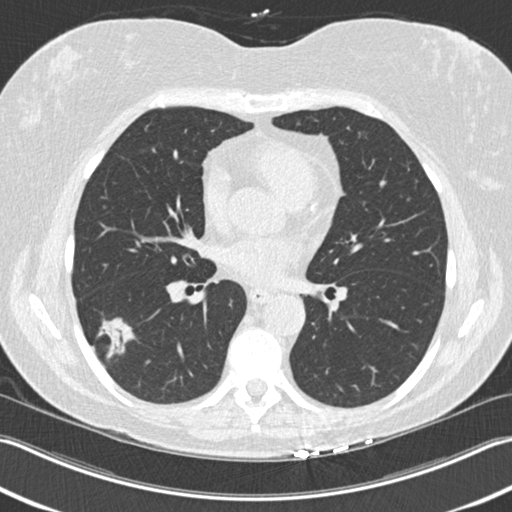
Low-dose screening chest CT, axial slice, baseline screening round, lung window (W 1500 / L -600 HU), 2 mm slice thickness, slice 96 of 211 in the series, 512 × 512 image matrix. Female participant, aged 63 years at enrolment. Current smoker at enrolment.
Lesion marked by an expert reader, bounding box [x1, y1, x2, y2] px = [77, 314, 139, 371]. The screening reader recorded 3 non-calcified nodules or masses ≥4 mm on this exam (right upper lobe, right lower lobe, right lower lobe); which of them this box marks is not recorded. Official screen result: positive, change unspecified: nodule(s) >= 4 mm or enlarging nodule(s), mass(es), or other non-specific abnormalities suspicious for lung cancer. Participant outcome: lung cancer diagnosed 57 days after this screen — bronchiolo-alveolar adenocarcinoma, NOS, right lower lobe, well differentiated (G1), stage IA (AJCC 6th edition), 25 mm at pathology.